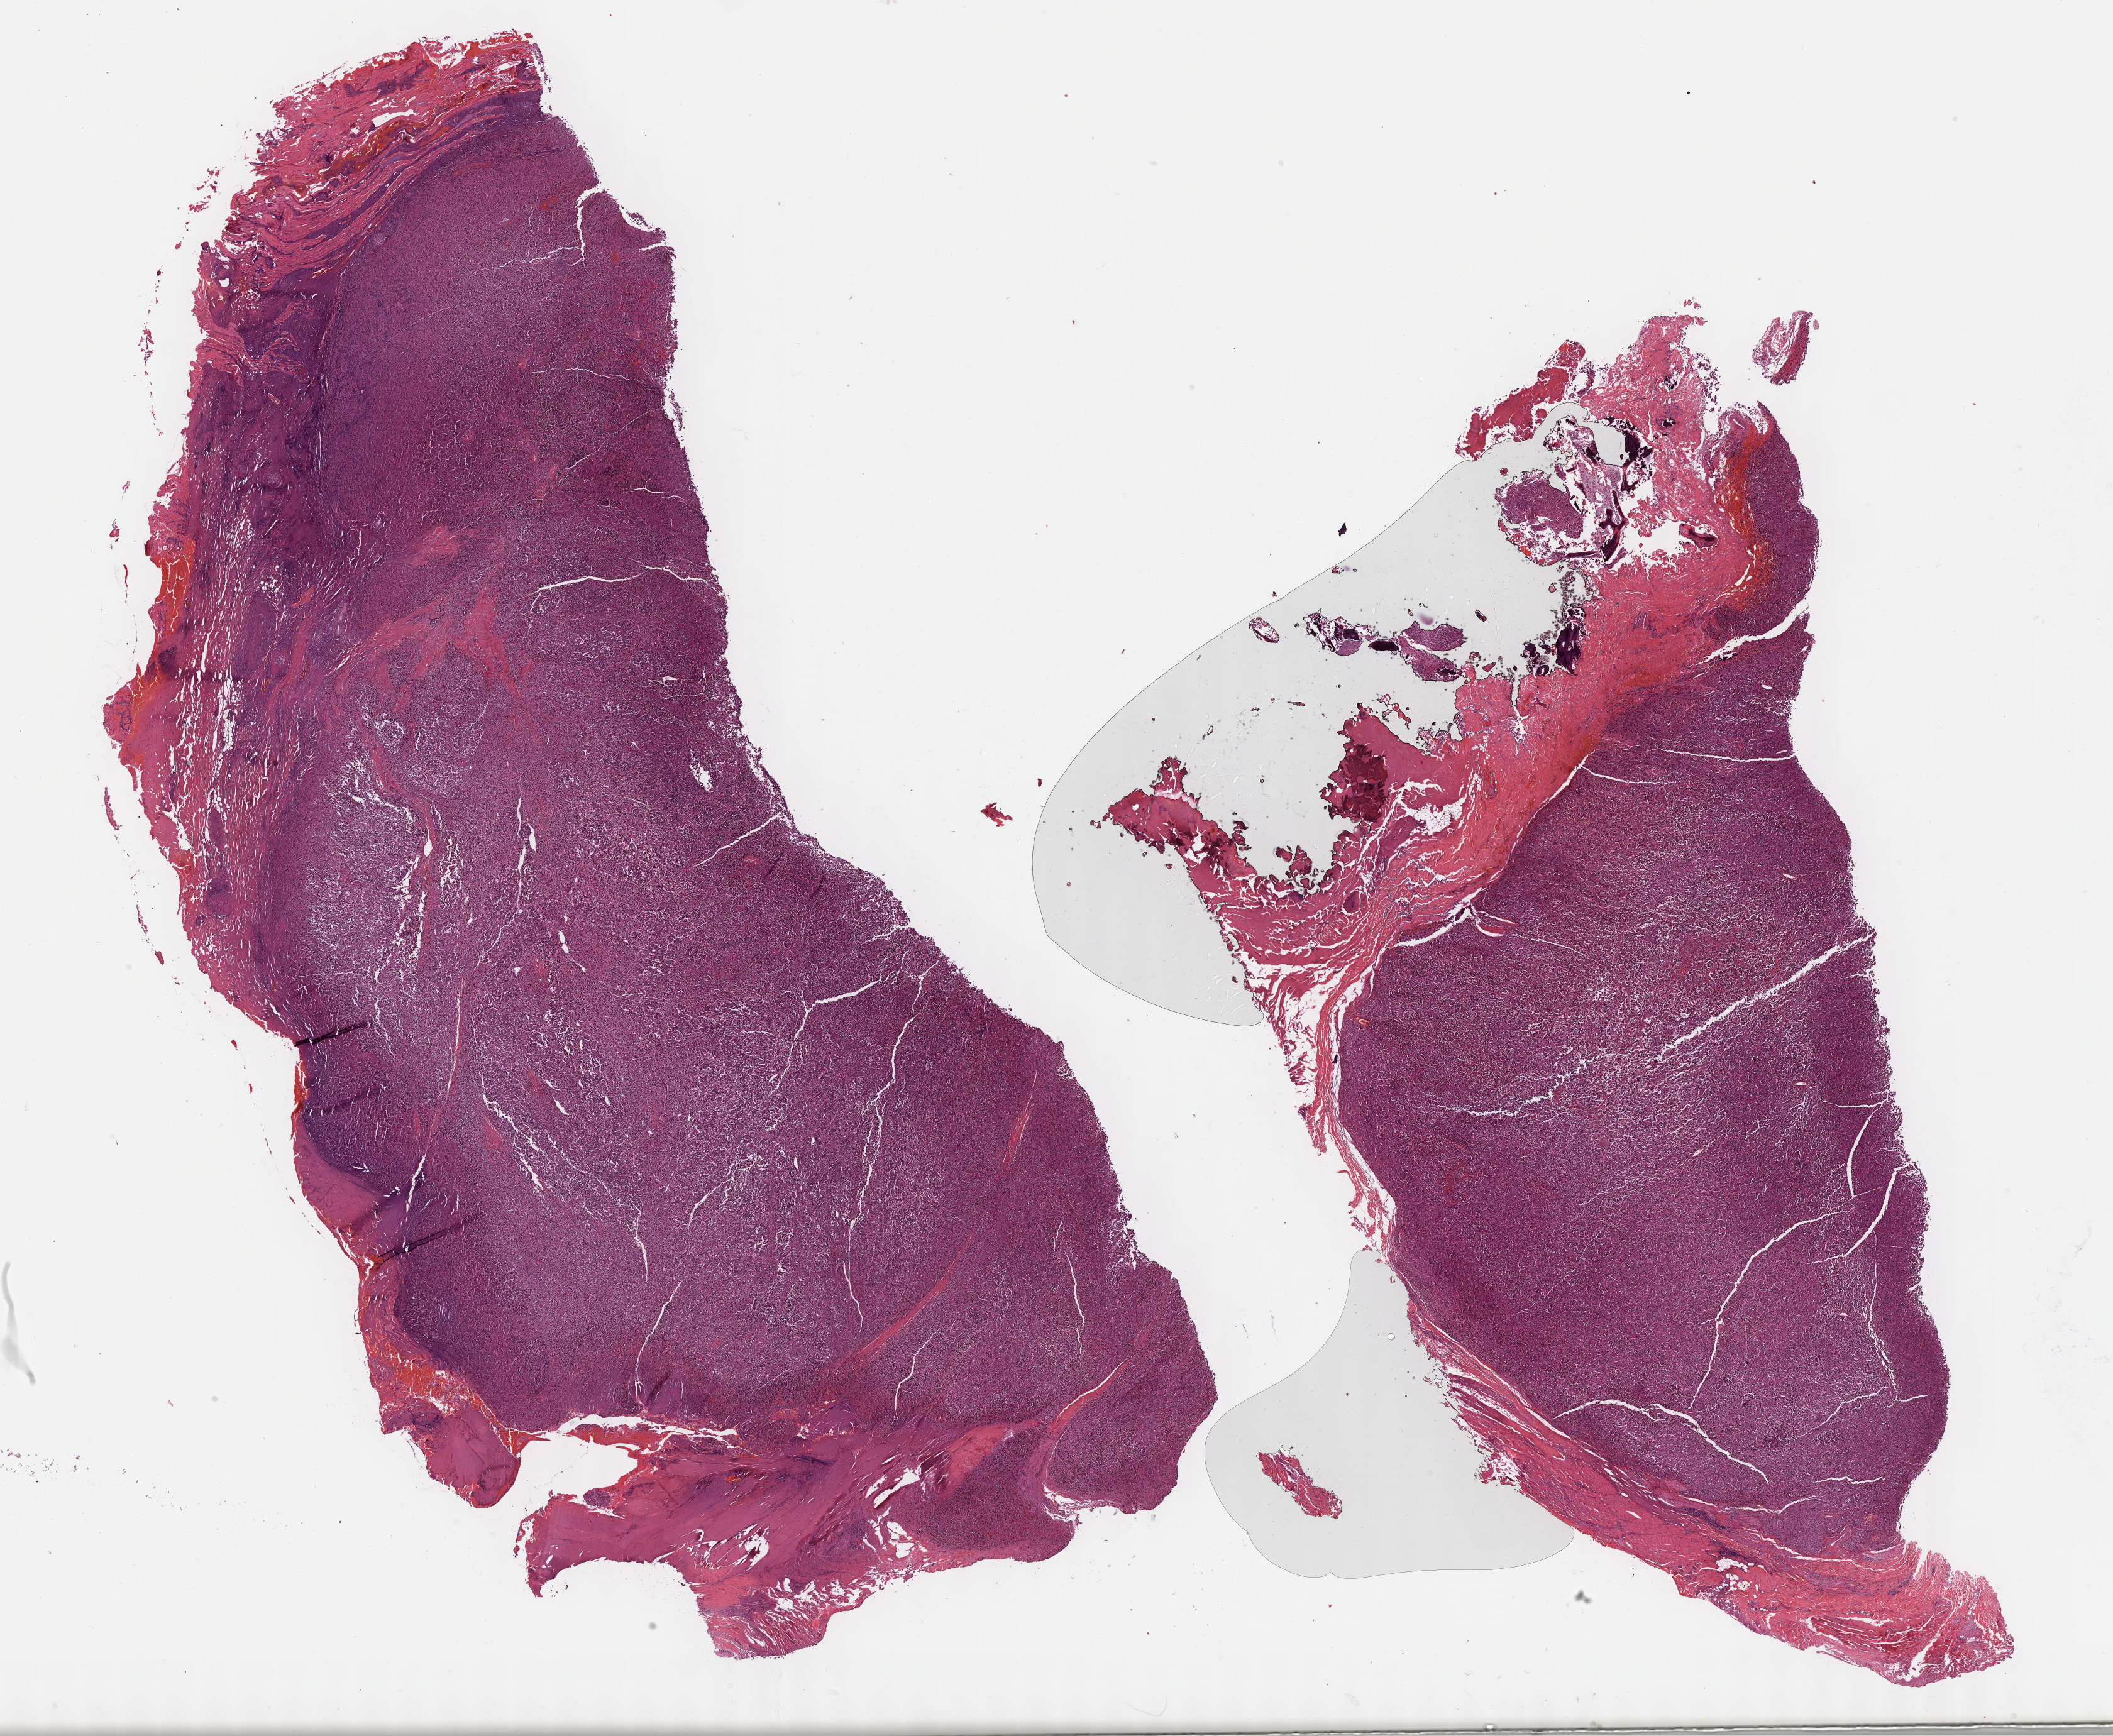
H&E-stained whole-slide image — whole scanned area (about 27.2 x 22.3 mm) shown as a low-resolution overview, formalin-fixed paraffin-embedded (FFPE) diagnostic section, sample: primary tumour, skin. Patient sex: female.
* pathologic diagnosis: Malignant melanoma, NOS